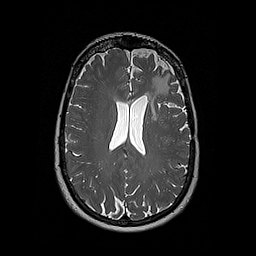
Brain MRI from a brain-tumour surgery series, one axial slice. Slice 114 of 192 in the series (ordered by position). 1 mm slice thickness. 256 × 256 image matrix, field of view 250 × 250 mm. From the clinical record (not read from this slice): histopathology: Oligodendroglioma; WHO grade: 2; IDH mutation: yes.
Annotated regions visible in this slice (outlined manually by an expert reader):
- tumour: box from (x=147, y=76) to (x=161, y=119) px